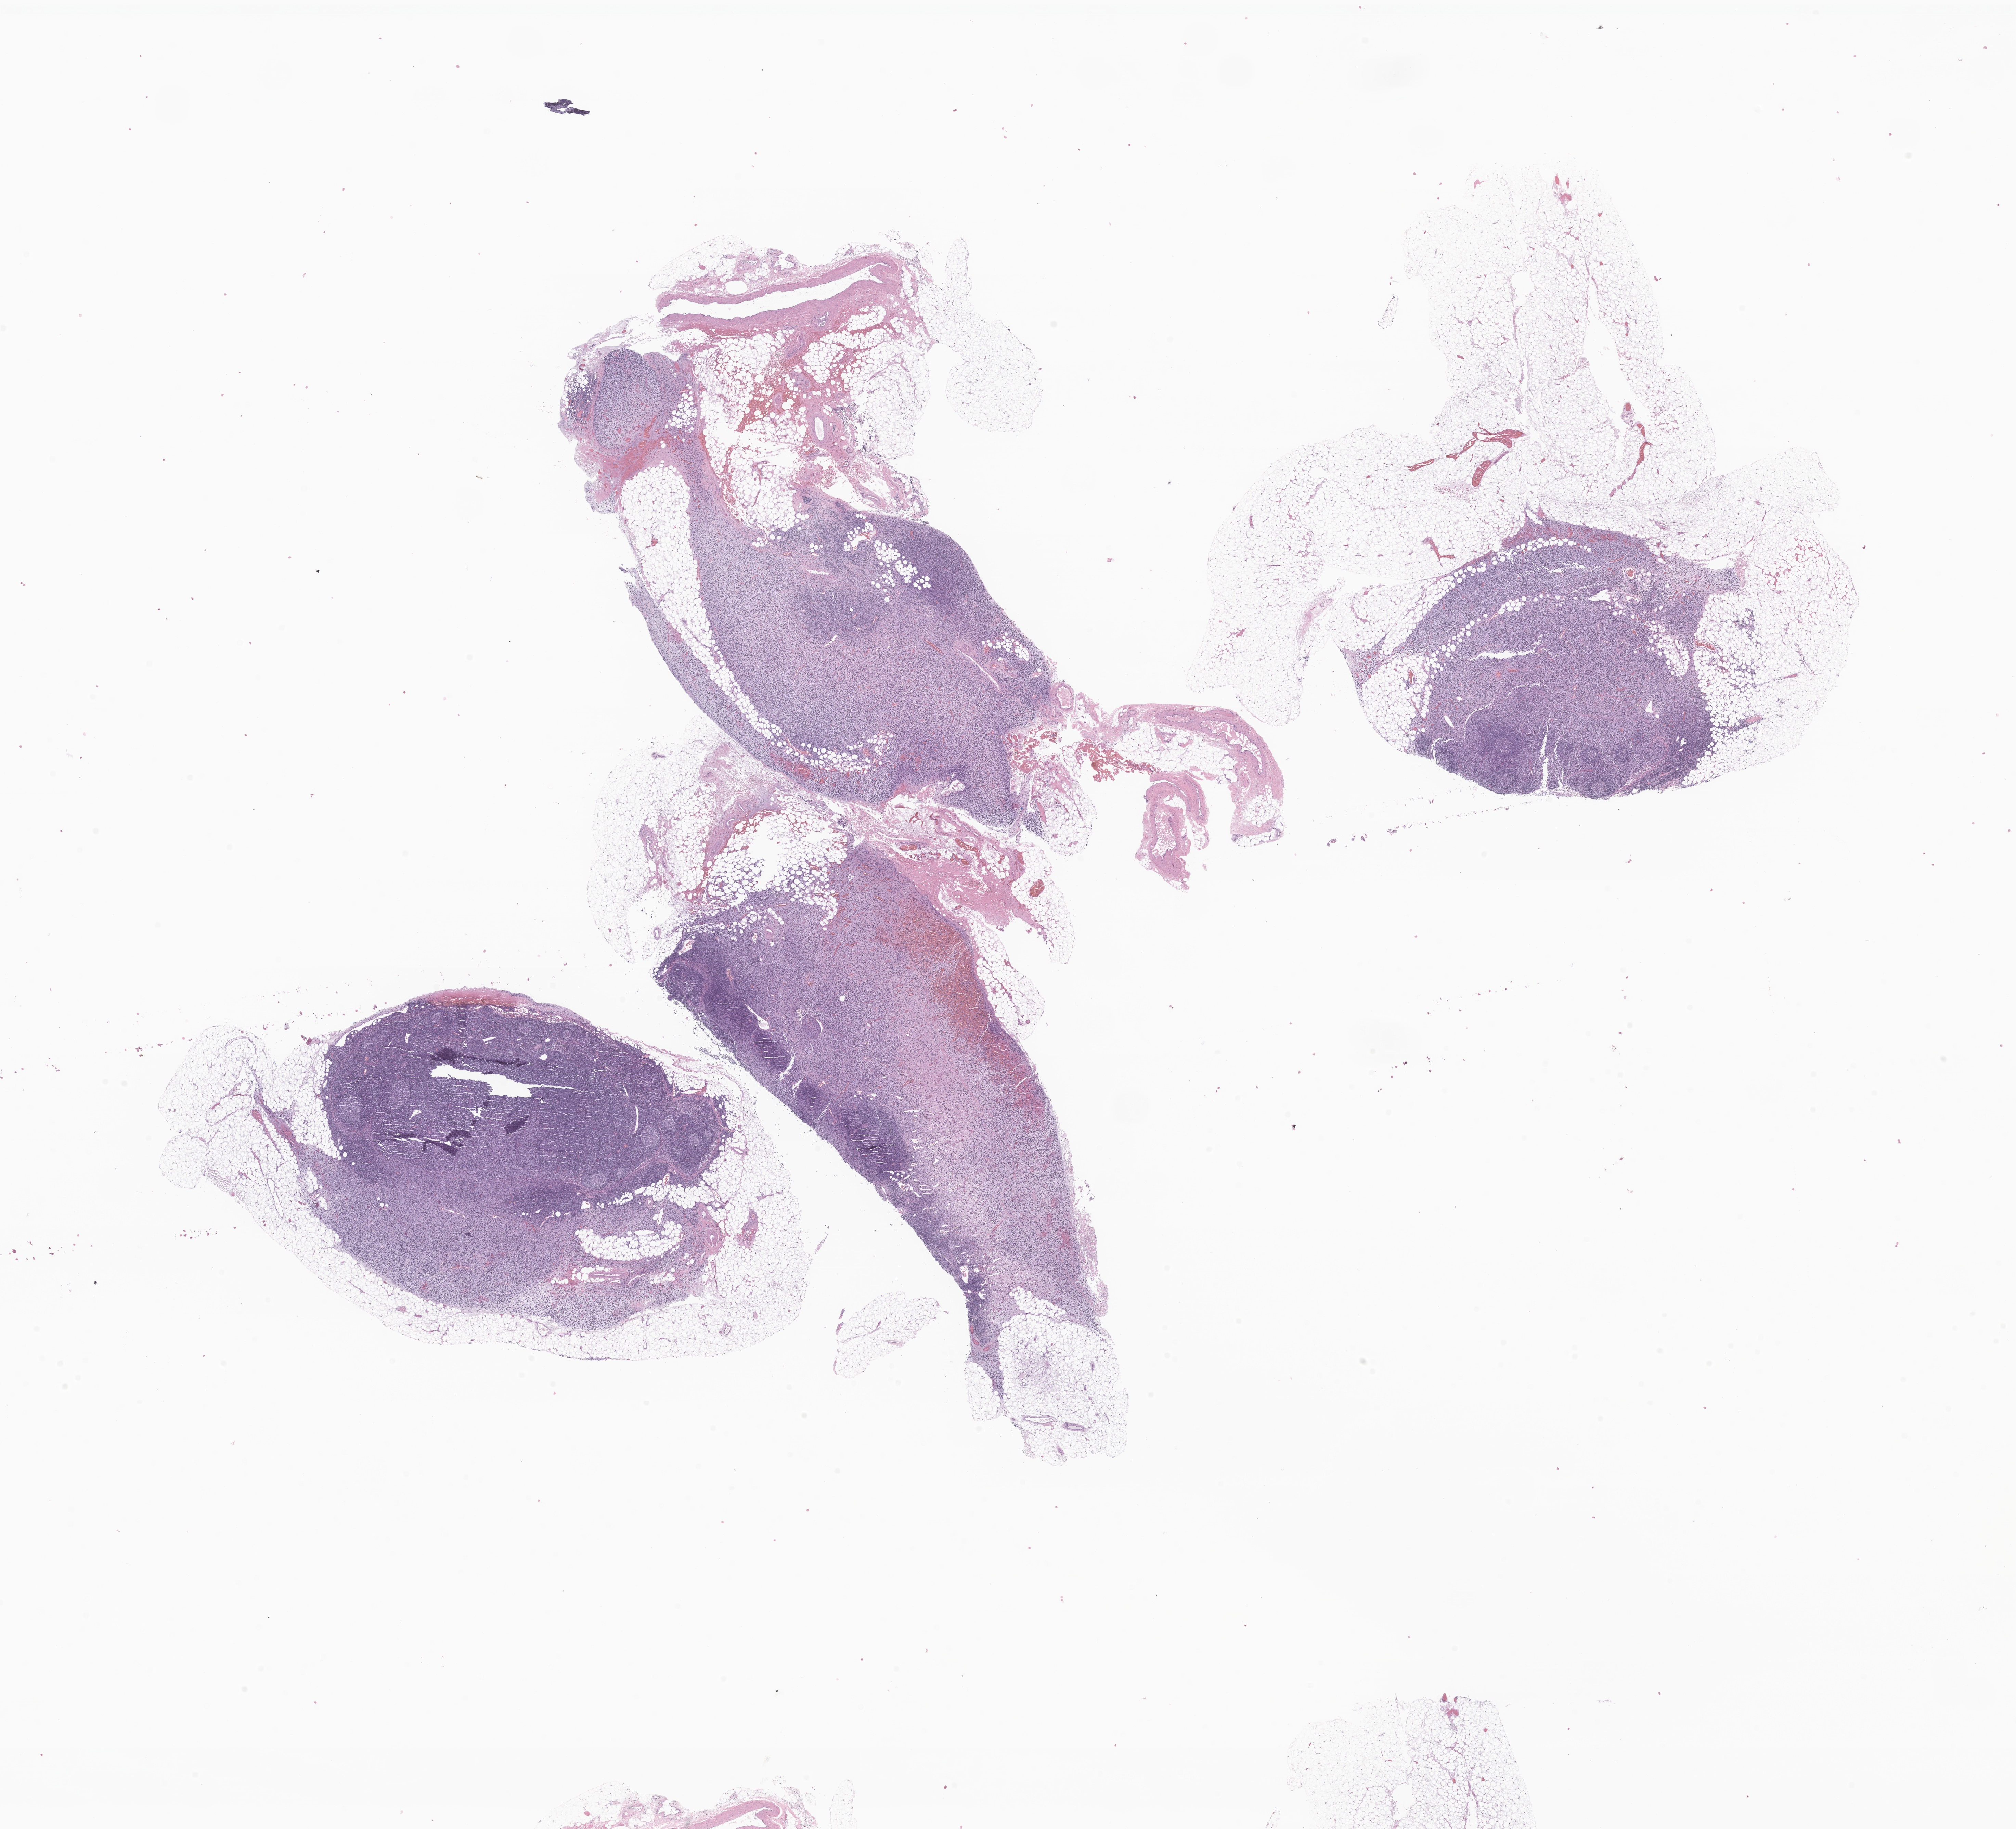
Whole-slide image, haematoxylin and eosin stain of tumor tissue from the testis, a low-resolution overview of the entire scanned area, about 24.8 x 22.5 mm; formalin-fixed, paraffin-embedded (FFPE) tissue. Patient: male, age 205 months.
Recorded diagnosis: Rhabdomyosarcoma, NOS.